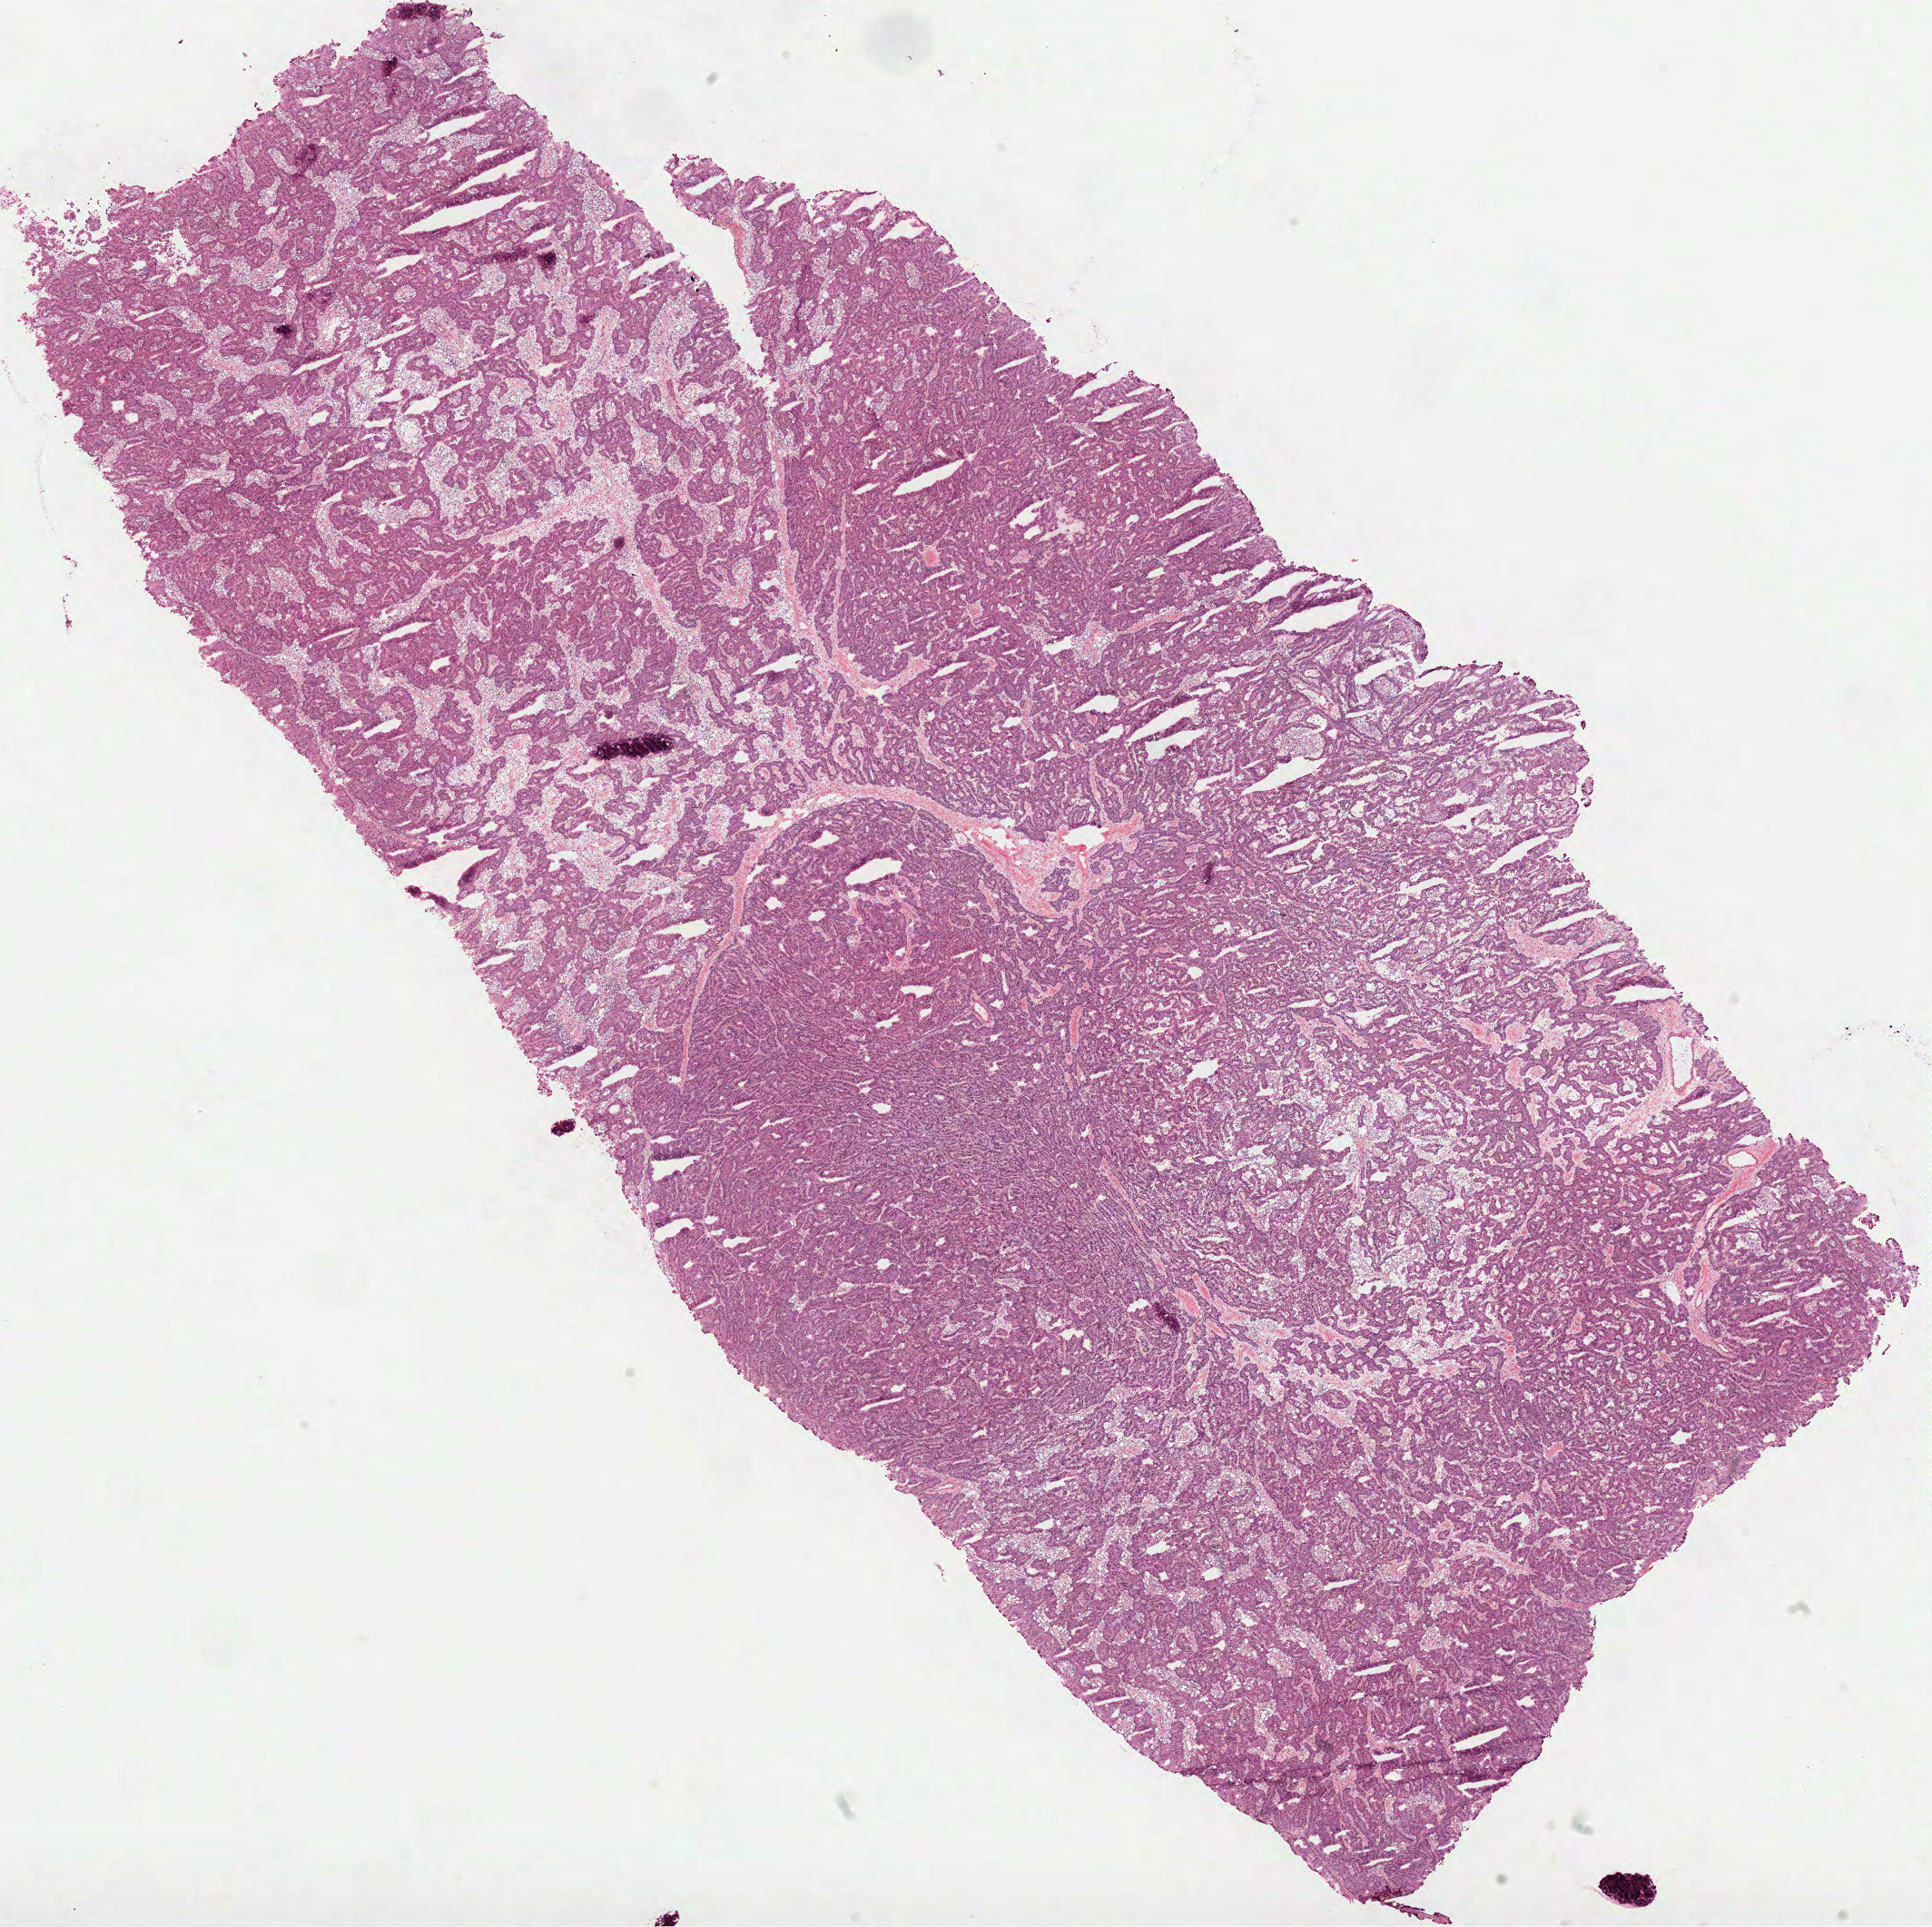
Whole-slide histology image, H&E — shown as a low-resolution overview of the whole scanned area (about 17.2 x 17.1 mm, acquisition: 40x scan). Frozen section from the top of the tissue portion. Kidney, primary tumour sample. Patient: male, age at initial diagnosis 53 years. Composition of this section per pathologist review: tumour cells 100%, tumour nuclei 90%, normal cells 0%, stromal cells 0%, necrosis 0%. Inflammatory infiltration, as recorded: lymphocyte infiltration 0%, monocyte infiltration 5%, neutrophil infiltration 0%.
Laterality: right. Pathologic diagnosis: Papillary adenocarcinoma, NOS. AJCC pathologic stage: I.